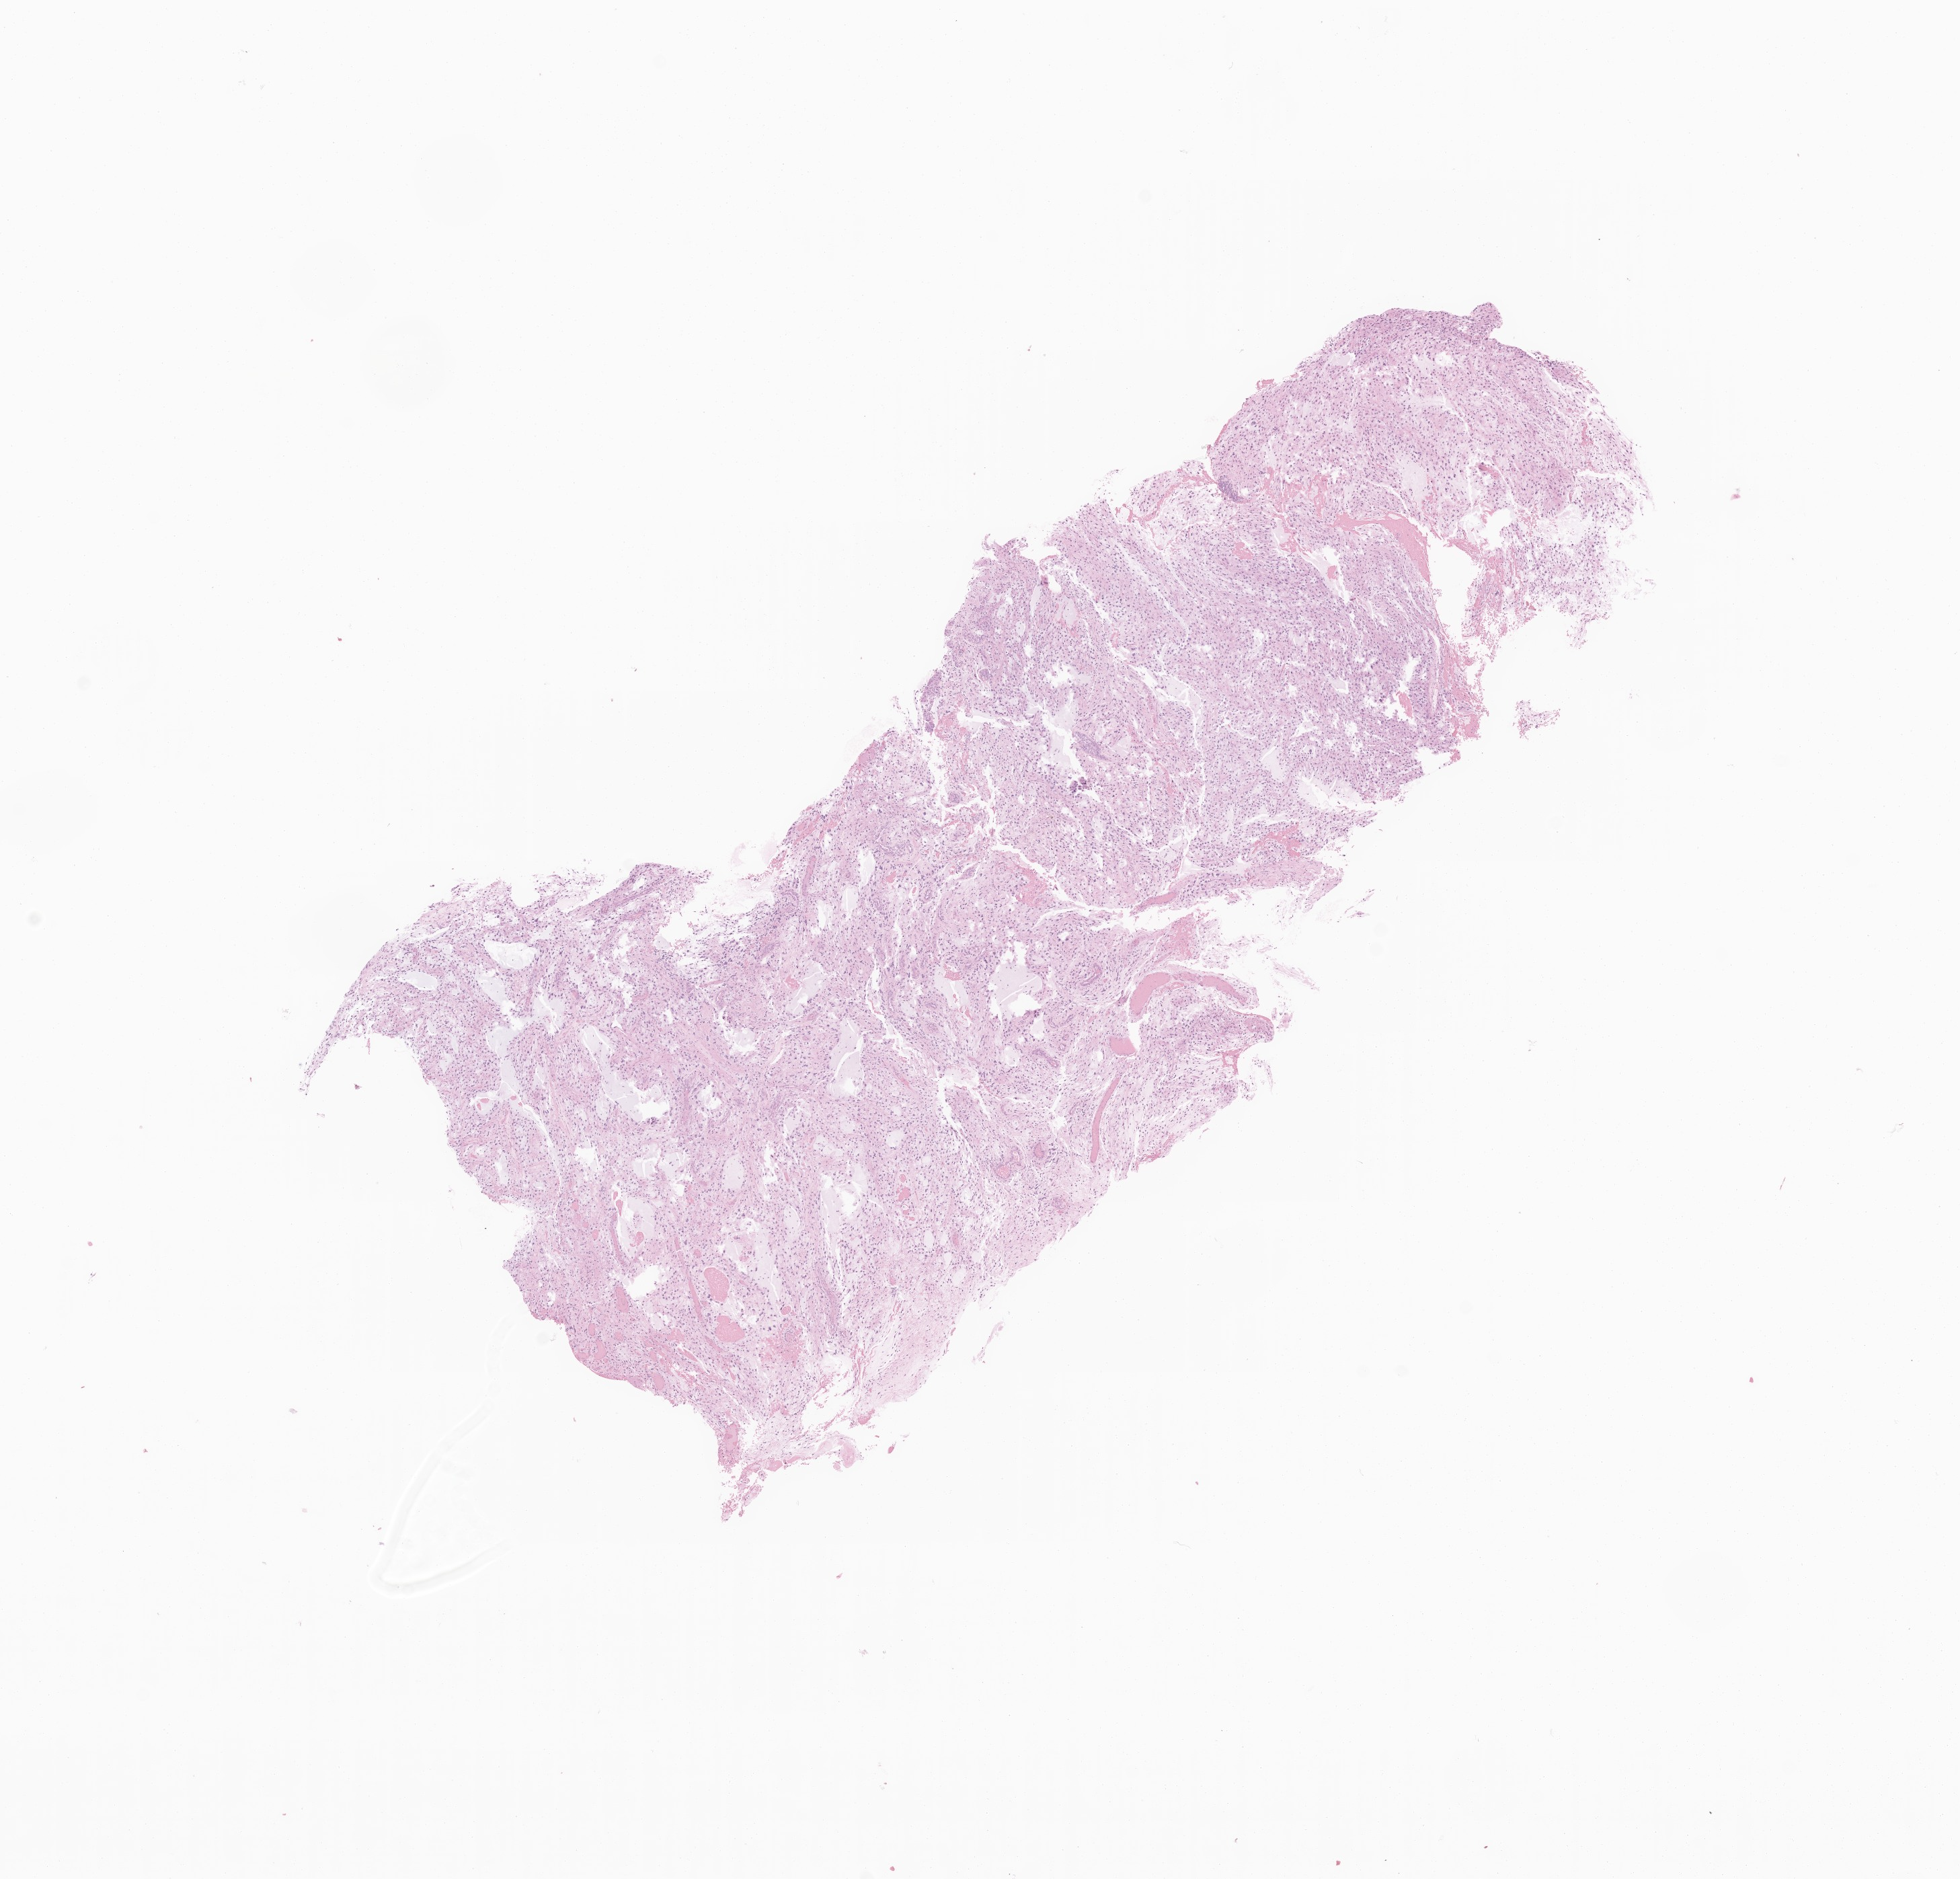
Digitized haematoxylin and eosin-stained section of tumor tissue from the brain stem — whole scanned area (about 12.3 x 11.8 mm) shown as a low-resolution overview, formalin-fixed, paraffin-embedded (FFPE) tissue. Patient: male, age 202 months (16 years 10 months).
- diagnosis: Pilocytic astrocytoma